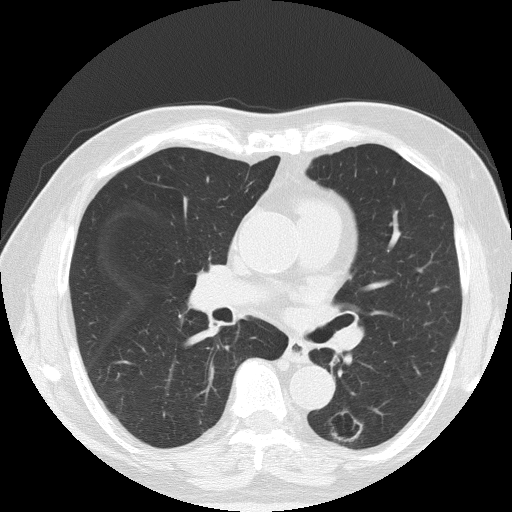
Low-dose screening chest CT, axial slice, baseline annual screen, lung window (W 1500 / L -600 HU), lung (sharp) reconstruction kernel (FC51), 120 kVp, 512 × 512 image matrix. Male participant, aged 71 years at enrolment. Former smoker at enrolment.
• Expert-annotated lung lesion, bounding box (x1, y1, x2, y2) in pixels: (321, 408, 373, 451).
• No non-calcified nodule or mass ≥4 mm was recorded by the screening reader at this exam.
• Official screen result: negative screen, significant abnormalities not suspicious for lung cancer.
• Lung cancer was diagnosed 340 days after this screen: adenocarcinoma, NOS, left lower lobe, poorly differentiated (G3), stage IA (AJCC 6th edition), 28 mm at pathology.